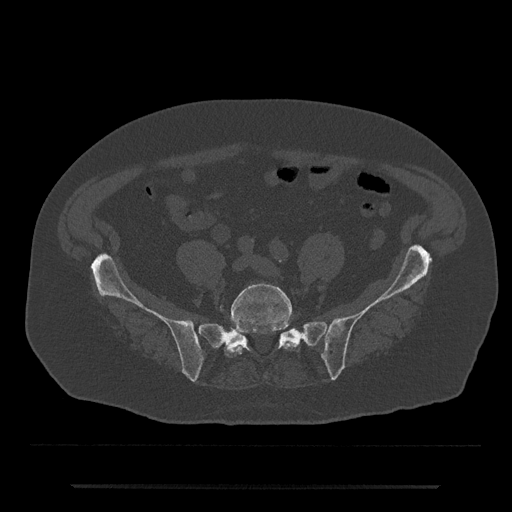
CT including the spine, one axial slice; position 264 of 797 along the scan axis; 120 kVp; bone window (W 1800 / L 400 HU); 512 × 512 image matrix, field of view 434 × 434 mm. Patient: male, 80 years. From the clinical record (not read from this slice): primary cancer: prostate; vertebrae with lytic lesions (as recorded): L1, T11.
Outlined on this slice (semi-automatically segmented with operator editing):
- L5 vertebra: bounding box [x1, y1, x2, y2] px = [224, 283, 296, 357]